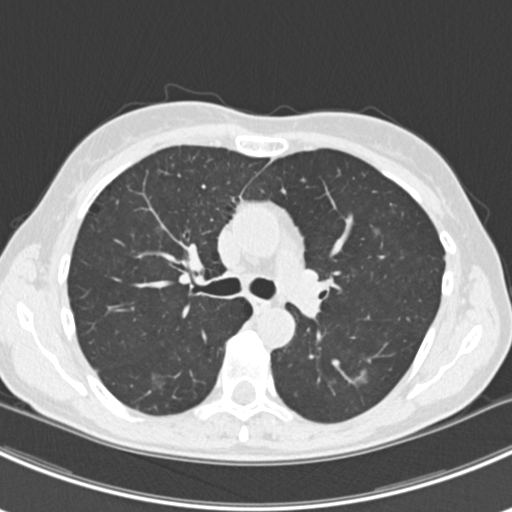
Low-dose screening chest CT, axial slice, first (baseline) screen, lung window (W 1500 / L -600 HU), 2 mm slice thickness, standard (soft-tissue) reconstruction kernel (B30f), slice 68 of 224 in the series. Female, age 63 years at enrolment. Current smoker at enrolment.
2 lesions marked by an expert reader on this slice (largest first), bounding box (x1, y1, x2, y2) in pixels: (135, 363, 179, 402); (344, 362, 383, 393). The screening reader recorded 10 non-calcified nodules or masses ≥4 mm on this exam (right lower lobe, right lower lobe, left lower lobe, left lower lobe, right middle lobe, right lower lobe, left lower lobe, left upper lobe, right upper lobe, left upper lobe); which of them these boxes mark is not recorded. Official screen result: positive, change unspecified: nodule(s) >= 4 mm or enlarging nodule(s), mass(es), or other non-specific abnormalities suspicious for lung cancer. Lung cancer was diagnosed 751 days after this screen: bronchiolo-alveolar adenocarcinoma, NOS, right upper lobe, right middle lobe, right lower lobe, left upper lobe, left lower lobe, moderately differentiated (G2), stage IV (AJCC 6th edition).